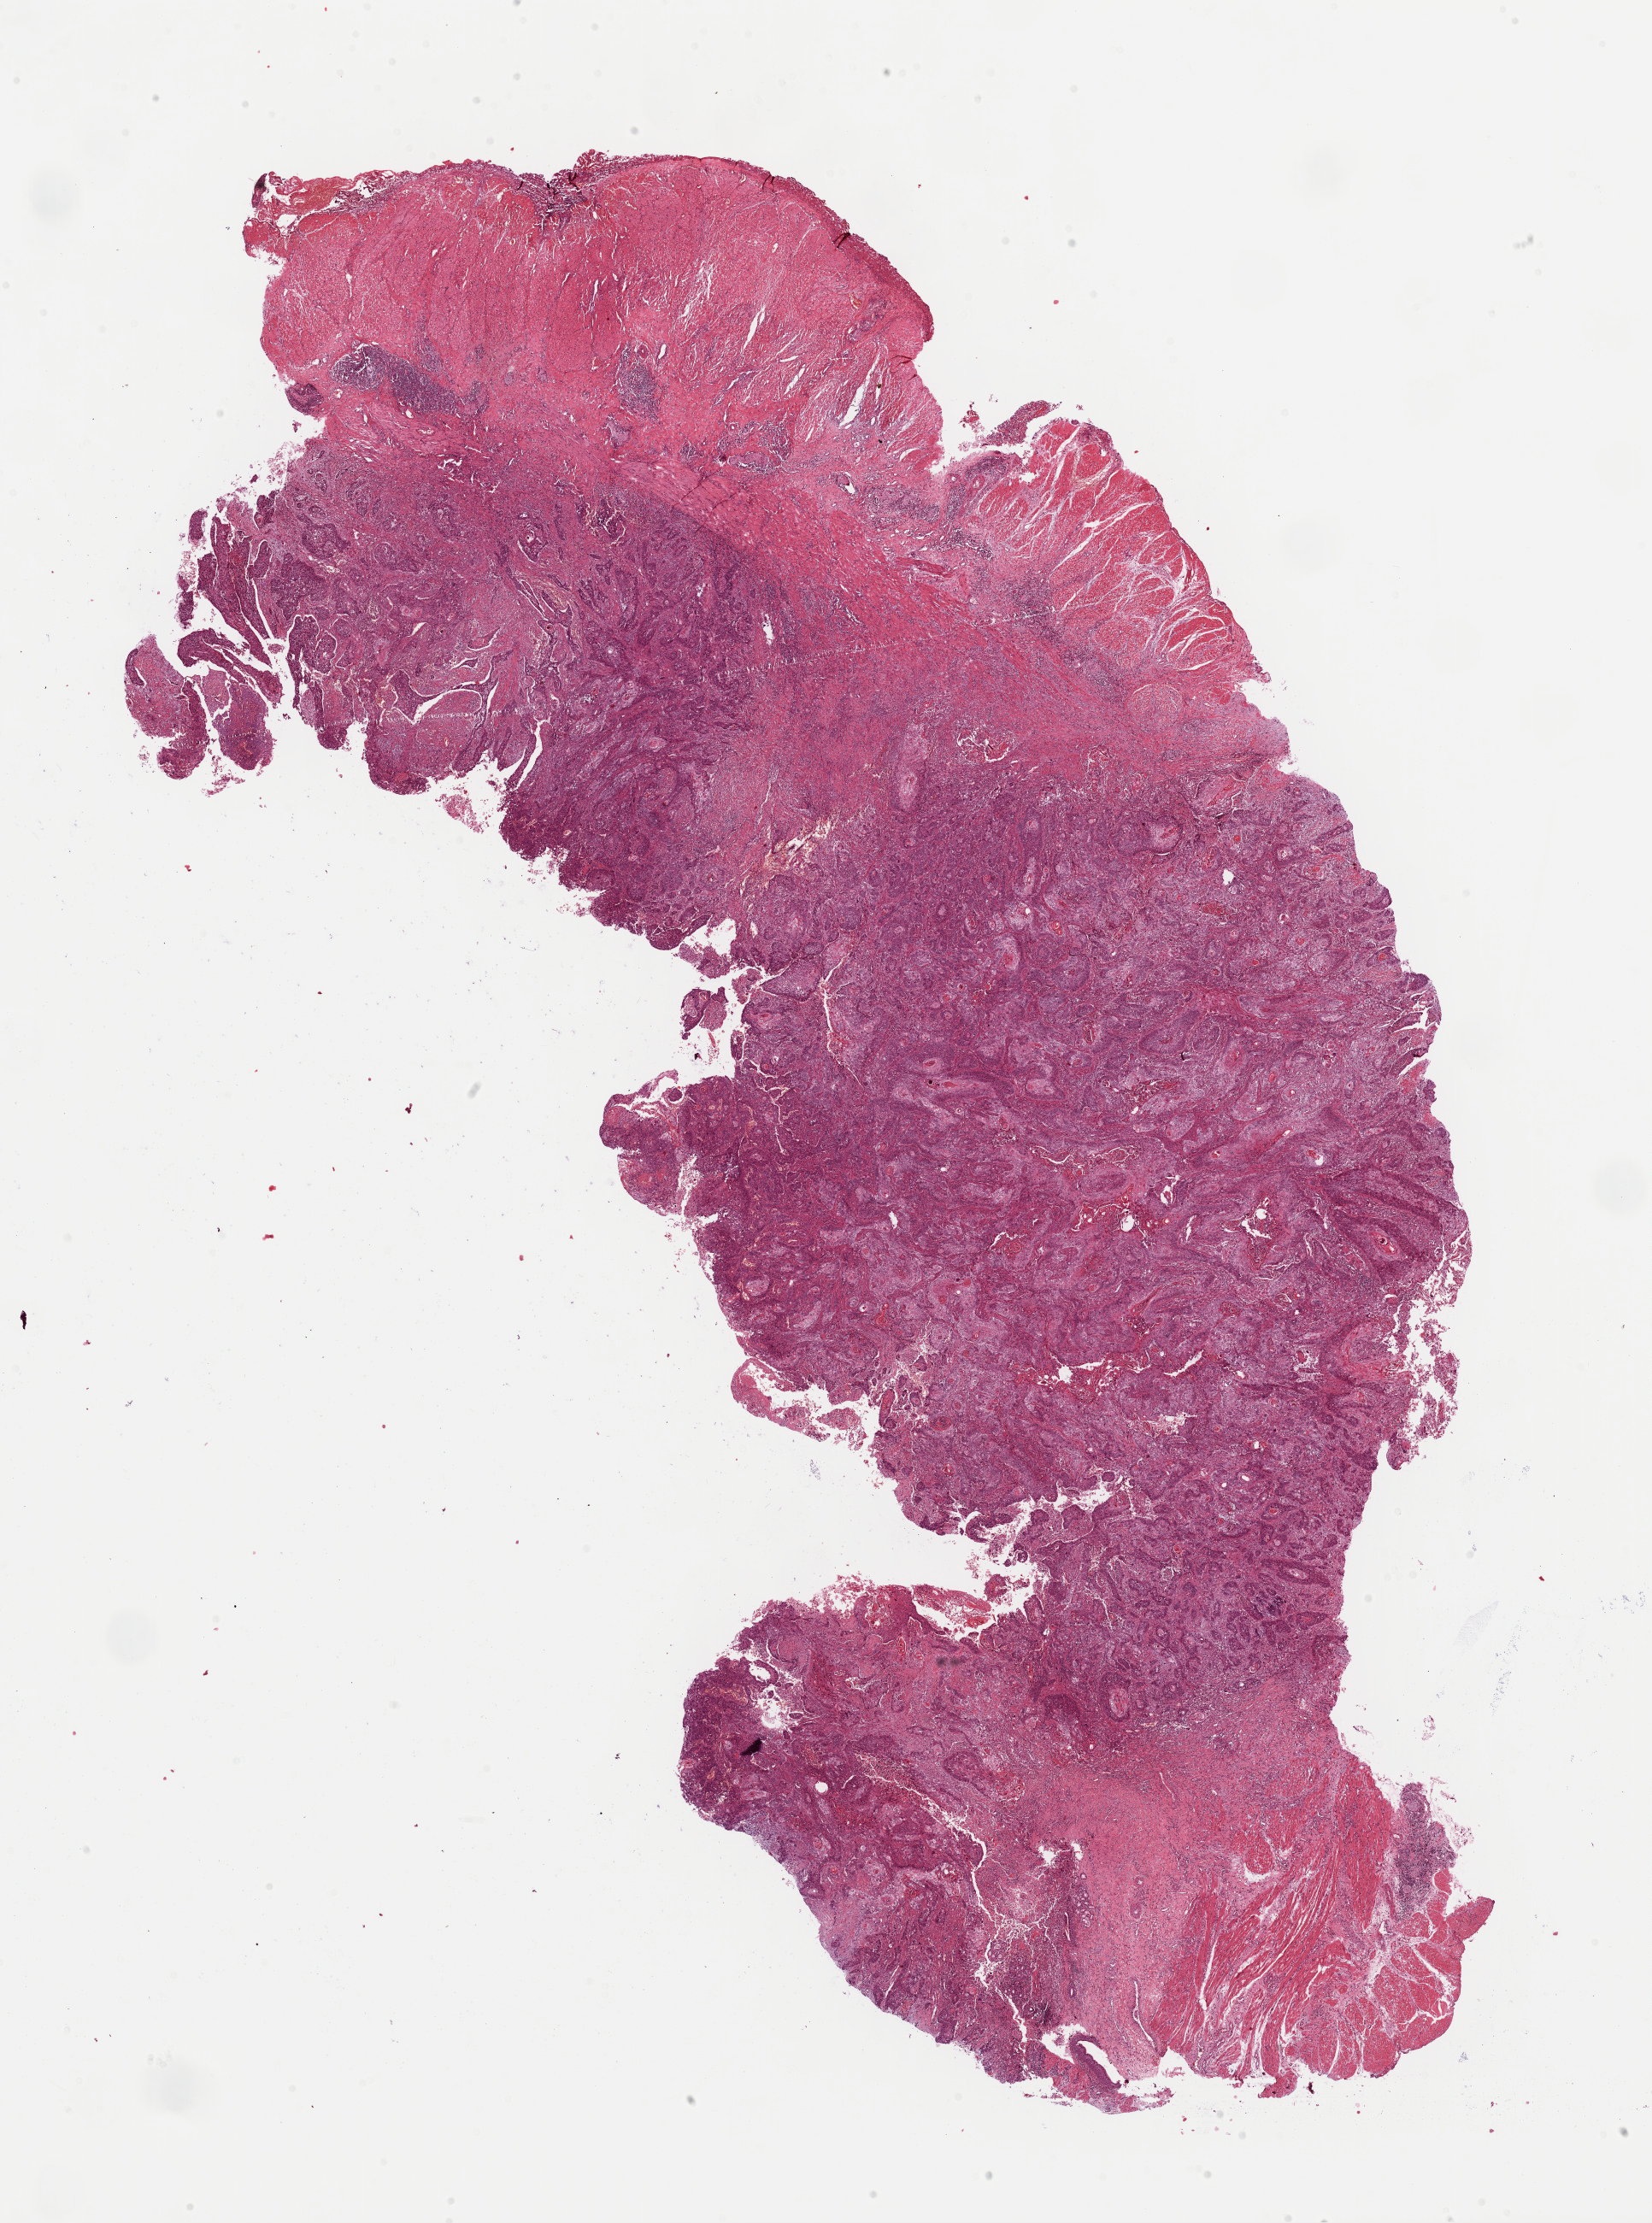
Digitized H&E-stained tissue section (whole slide), whole scanned area (about 15.3 x 20.5 mm) shown as a low-resolution overview; formalin-fixed paraffin-embedded (FFPE) diagnostic section; primary tumour sample from the esophagus. Male patient; age at initial diagnosis 44 years. Histologic grade: G2 (moderately differentiated).
• AJCC pathologic stage: IIA (6th edition)
• diagnosis: Squamous cell carcinoma, NOS (middle third of esophagus)